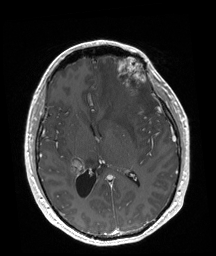
Brain MRI from a brain-tumour surgery series, one axial slice; position 91 of 192 along the scan axis; T1-weighted post-contrast; 1 mm slice thickness; 216 × 256 image matrix, field of view 219 × 260 mm.
Structures marked on this image (manually delineated by an expert):
- tumour: box from (x=116, y=56) to (x=146, y=98) px